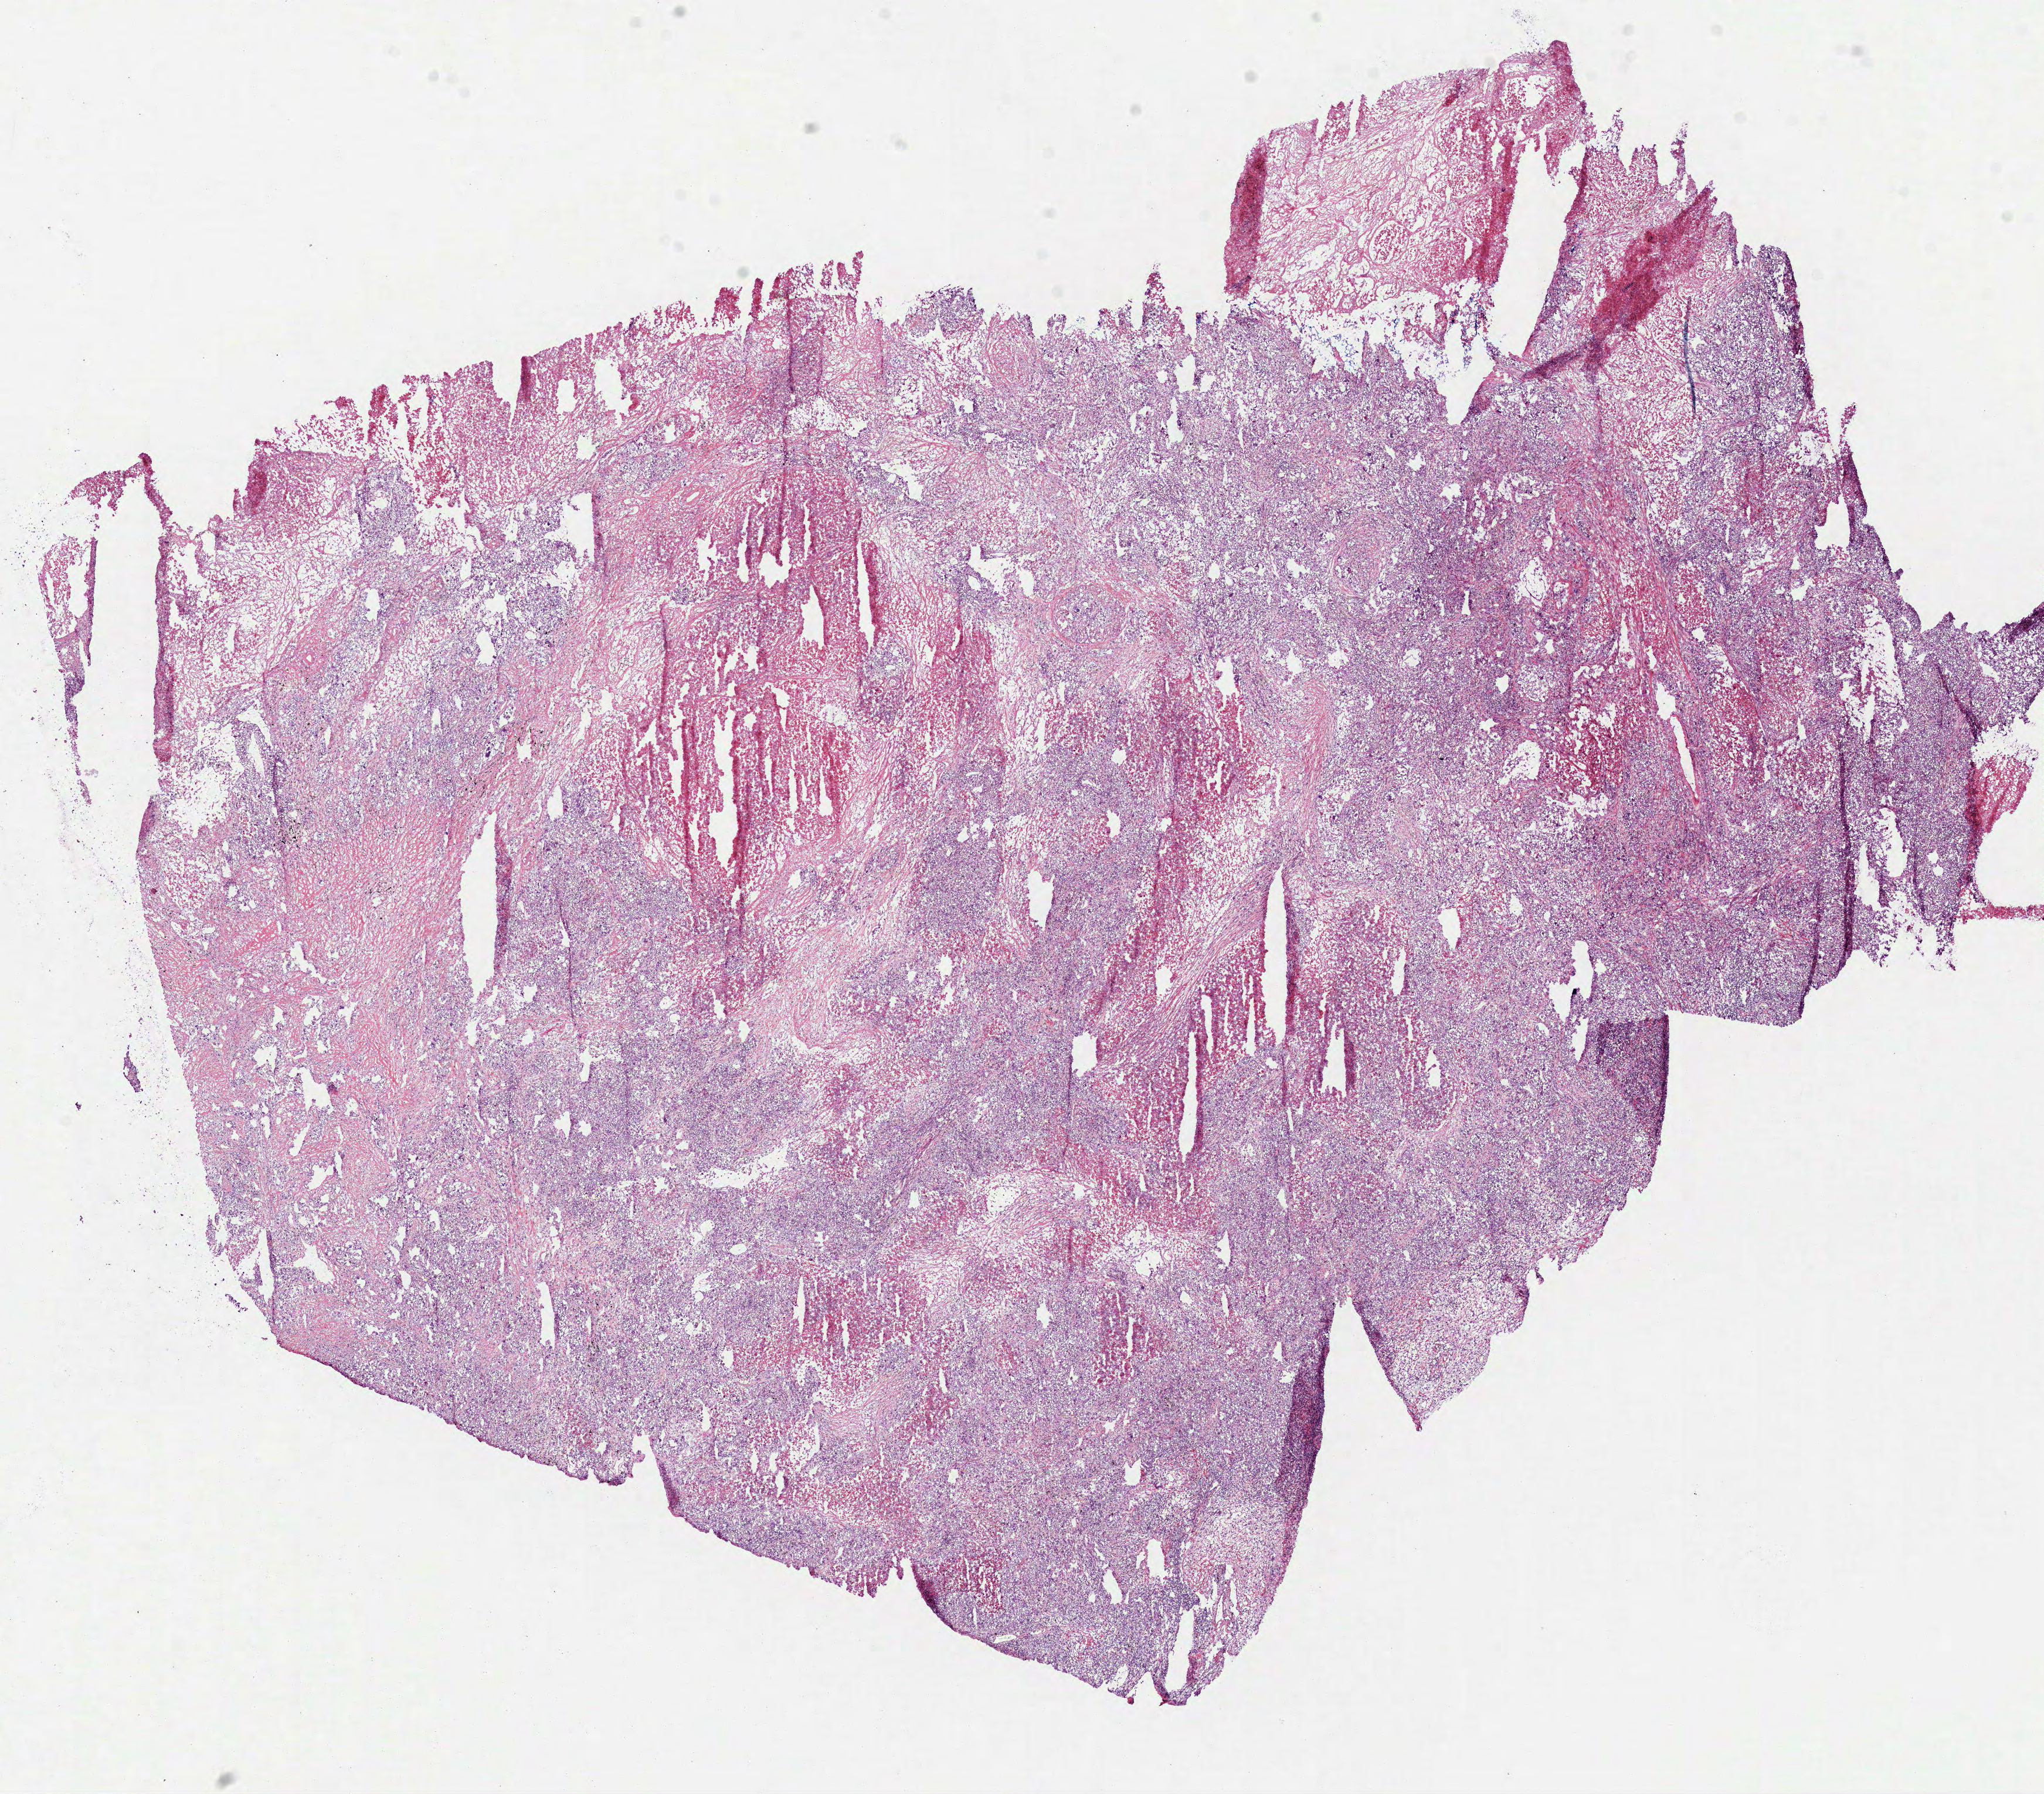
Digitized Hematoxylin and eosin (H&E) stained tissue section (whole slide) — shown as a low-resolution overview of the whole scanned area (about 14.1 x 12.3 mm, acquisition: 40x scan), frozen section from the top of the tissue portion, lung, primary tumour sample. Female patient; age at initial diagnosis 71 years. Slide review estimates, as recorded: tumour cells 65%, tumour nuclei 80%, normal cells 0%, stromal cells 15%, necrosis 20%.
- AJCC pathologic stage: IB (6th edition)
- laterality: left
- diagnosis: Adenocarcinoma, NOS (lower lobe, lung)
- TNM: T2 N0 M0